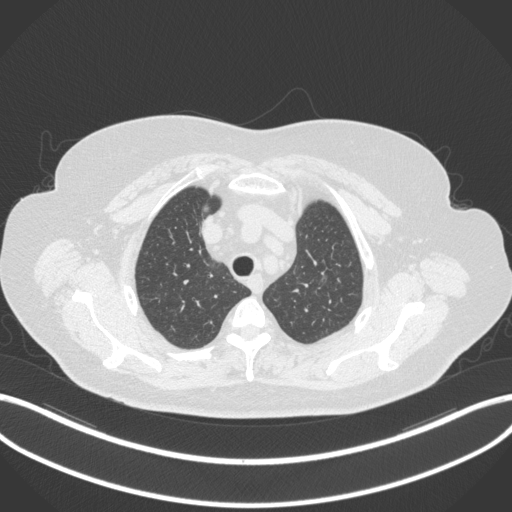
Chest CT, one axial slice. Slice 276 of 310 in the series (ordered by position). Lung window (W 1500 / L -600 HU). 1 mm slice thickness. 512 × 512 image matrix, field of view 400 × 400 mm. Patient: female, 70 years. From the clinical record (not read from this slice): clinical TNM (as recorded): T1c N0 M0.
Outlined on this slice (rectangle marked by the reading radiologist):
- lung tumour (recorded histology: adenocarcinoma): bounding box <316,265,330,290> (left, top, right, bottom; pixels)